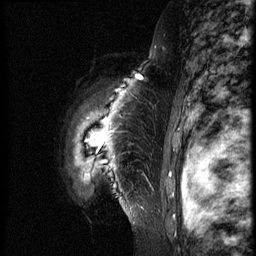
Breast MRI (dynamic contrast-enhanced), one sagittal slice; slice 56 of 66 in the series (ordered by position); dynamic contrast-enhanced series, image 2 of 3 at this slice position (ordered by acquisition); 1.5 T; TE 4.2 ms, TR 8.9 ms; 256 × 256 image matrix, field of view 200 × 200 mm. Patient: female, 39 years. Case-level facts recorded for this patient, not image findings: setting: breast cancer imaged before/during neoadjuvant chemotherapy; receptor status: HER2-positive.
Structures marked on this image (semi-automatic segmentation, software-assisted and operator-edited):
- analysis volume of interest (the breast-tissue region the enhancement analysis was run in; not a lesion): bounding box (x1, y1, x2, y2) in pixels: (59, 75, 163, 218)
- tumour enhancement mask (voxels above the 140 % enhancement threshold inside the analysis volume of interest): (139, 77, 143, 80)